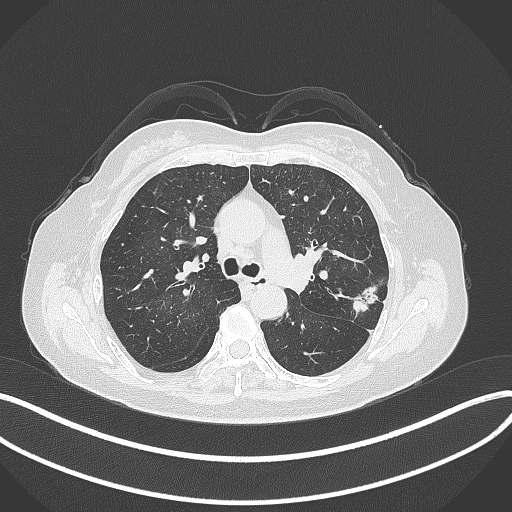
Chest CT, one axial slice. Position 208 of 319 along the scan axis. Reconstruction kernel B70f. Lung window (W 1500 / L -600 HU). 1 mm slice thickness. 512 × 512 image matrix. Female patient, age 60 years. From the clinical record (not read from this slice): clinical TNM (as recorded): T1c N0 M0.
Structures marked on this image (bounding box drawn by a radiologist):
- lung tumour (recorded histology: adenocarcinoma): bounding box (x1, y1, x2, y2) in pixels: (344, 277, 379, 319)